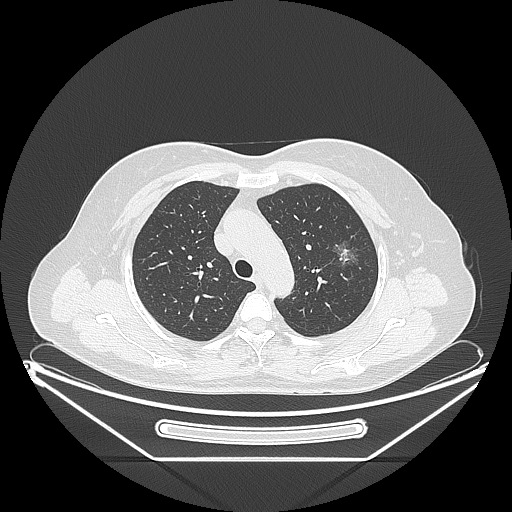
Chest CT, one axial slice. Lung window (W 1500 / L -600 HU). 1.25 mm slice thickness. 512 × 512 image matrix. Patient: female, 54 years. Case-level facts recorded for this patient, not image findings: clinical TNM (as recorded): T1c N0 M0.
Outlined on this slice (bounding box drawn by a radiologist):
- lung tumour (recorded histology: adenocarcinoma): bounding box <321,230,367,288> (left, top, right, bottom; pixels)